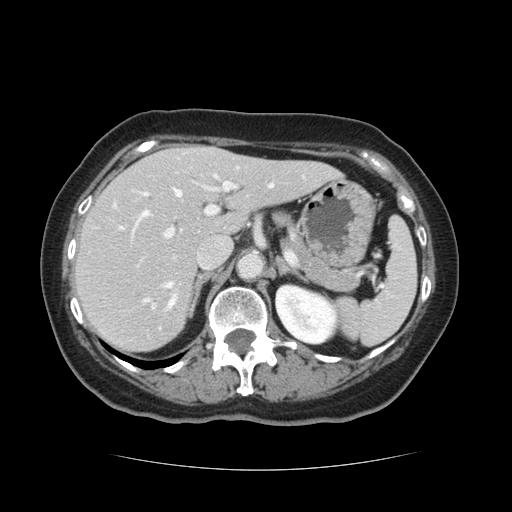
Contrast-enhanced abdominal CT, one axial slice. Slice 78 of 128 in the series (ordered by position). 120 kVp. Intravenous contrast given. Soft-tissue window (W 400 / L 40 HU). 512 × 512 image matrix. Female patient, age 67 years. Case-level facts recorded for this patient, not image findings: diagnosis: colorectal cancer liver metastases, imaged before liver resection; multiple liver metastases: yes; largest metastasis: 3 cm; chemotherapy before resection: no.
Outlined on this slice (outlined manually by an expert reader):
- hepatic veins: bounding box <140,185,273,309> (left, top, right, bottom; pixels)
- liver: <74,146,337,352>
- planned liver remnant (the part of the liver to remain after resection): <74,158,337,352>
- portal vein (with intrahepatic branches): <118,173,237,309>